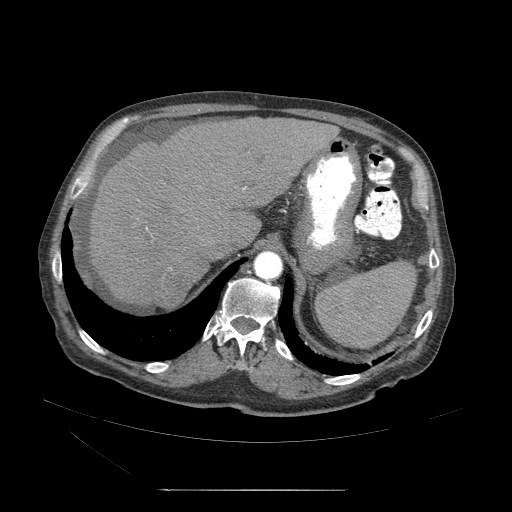
Contrast-enhanced abdominal CT (liver protocol), one axial slice; slice 38 of 71 in the series (ordered by position); reconstruction kernel STANDARD; 120 kVp; soft-tissue window (W 400 / L 40 HU); 512 × 512 image matrix, field of view 440 × 440 mm. From the clinical record (not read from this slice): diagnosis: hepatocellular carcinoma (patient treated with transarterial chemoembolisation; whether this scan precedes or follows treatment is not stated here); TNM stage (as recorded): Stage-II; Child-Pugh class: A; tumour nodularity: multinodular; tumour size: 1 cm.
Structures marked on this image (semi-automatic segmentation, software-assisted and operator-edited):
- abdominal aorta: box from (x=253, y=252) to (x=284, y=281) px
- liver parenchyma outside the tumour (the mass and vessels are separate outlines, so this box may not span the whole liver): (x=80, y=119)–(x=340, y=314)
- mass: (x=154, y=287)–(x=184, y=309)
- liver vessels: (x=129, y=162)–(x=233, y=263)